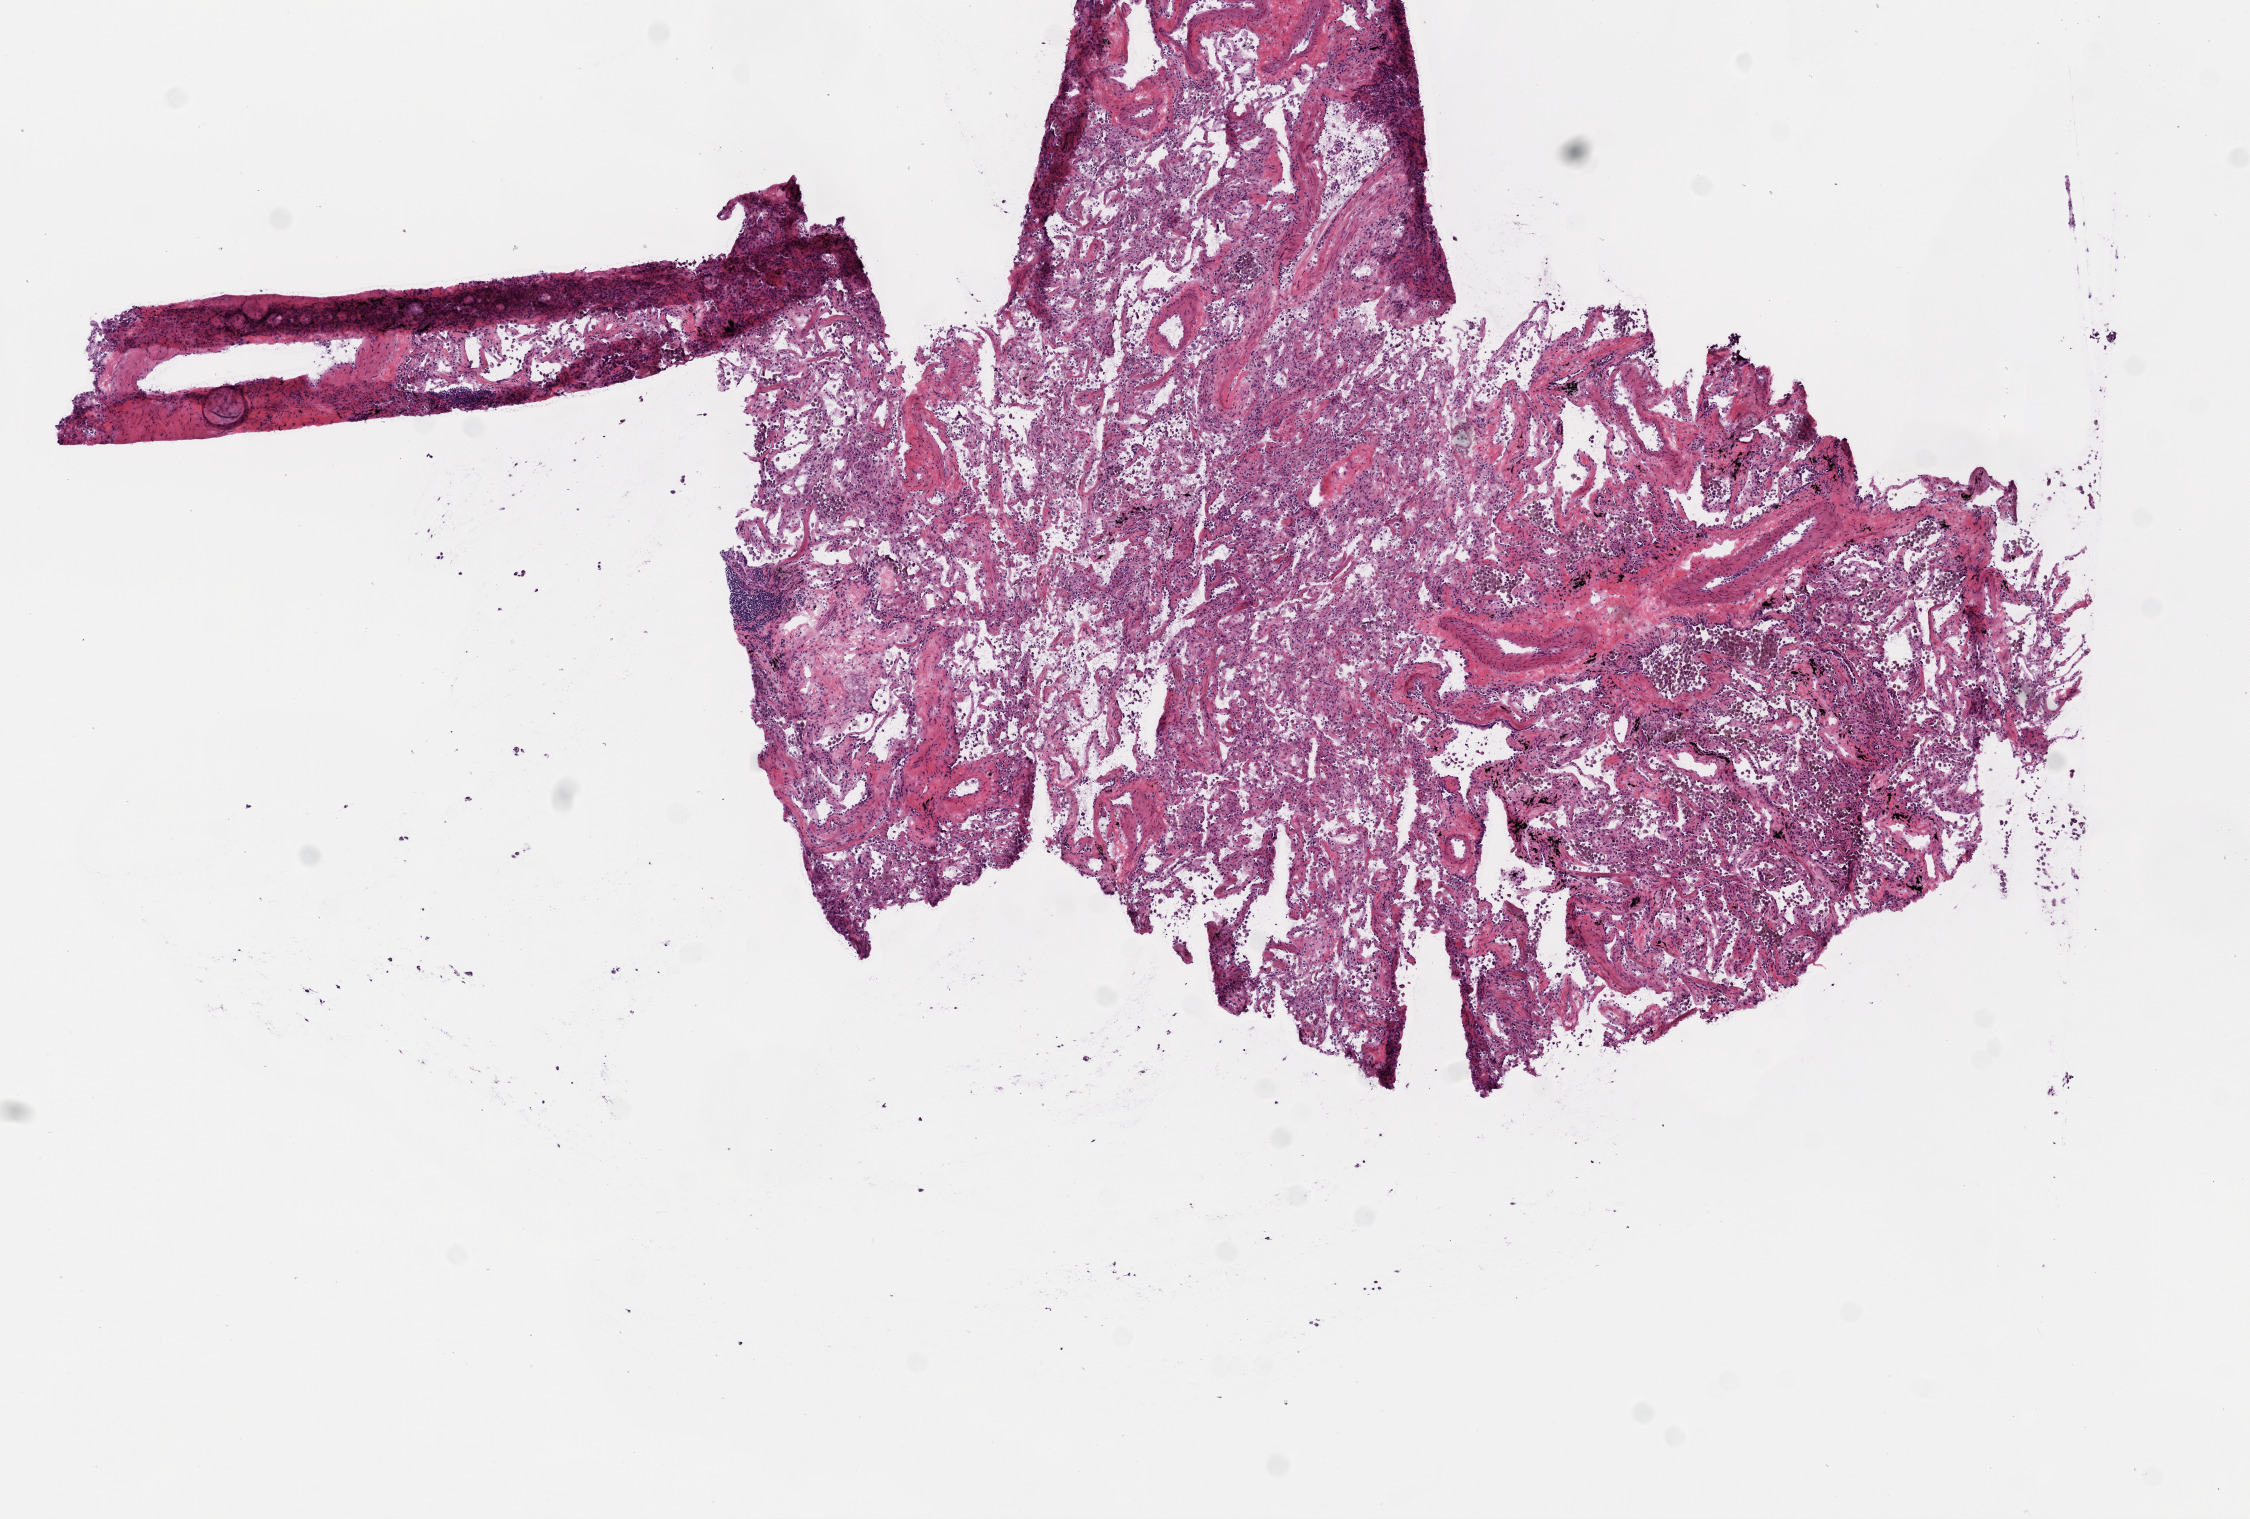
H&E-stained whole-slide image — whole scanned area (about 9.0 x 6.1 mm, from a 20x scan) shown as a low-resolution overview; frozen section from the top of the tissue portion; solid tissue normal (non-tumour tissue) sample from the lung. Female, age 66 years at initial diagnosis.
* this section: solid tissue normal sample (biorepository sample class)
* patient diagnosis: Adenocarcinoma, NOS (upper lobe, lung)